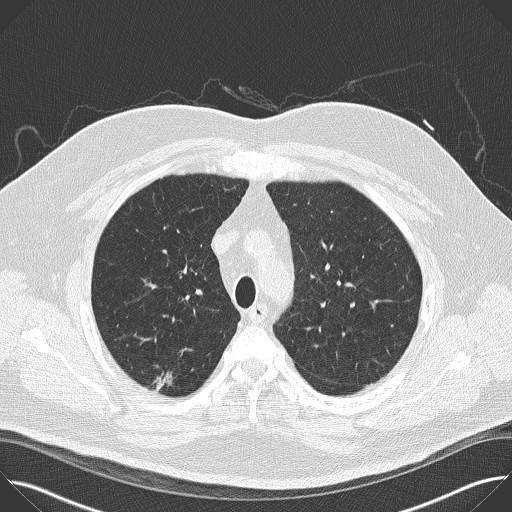
Chest CT (low-dose screening protocol), one axial image, baseline annual screen, lung window (W 1500 / L -600 HU), 2 mm slice thickness, 512 × 512 image matrix, field of view 380 × 380 mm. Male participant, aged 65 years at enrolment.
- Expert-annotated lung lesion, box from (x=137, y=362) to (x=189, y=404) px.
- The screening reader recorded 2 non-calcified nodules or masses ≥4 mm on this exam (right upper lobe, right upper lobe); which of them this box marks is not recorded.
- Lung cancer was diagnosed 47 days after this screen: bronchiolo-alveolar adenocarcinoma, NOS, right upper lobe, moderately differentiated (G2), stage IIA (AJCC 6th edition), 14 mm at pathology.